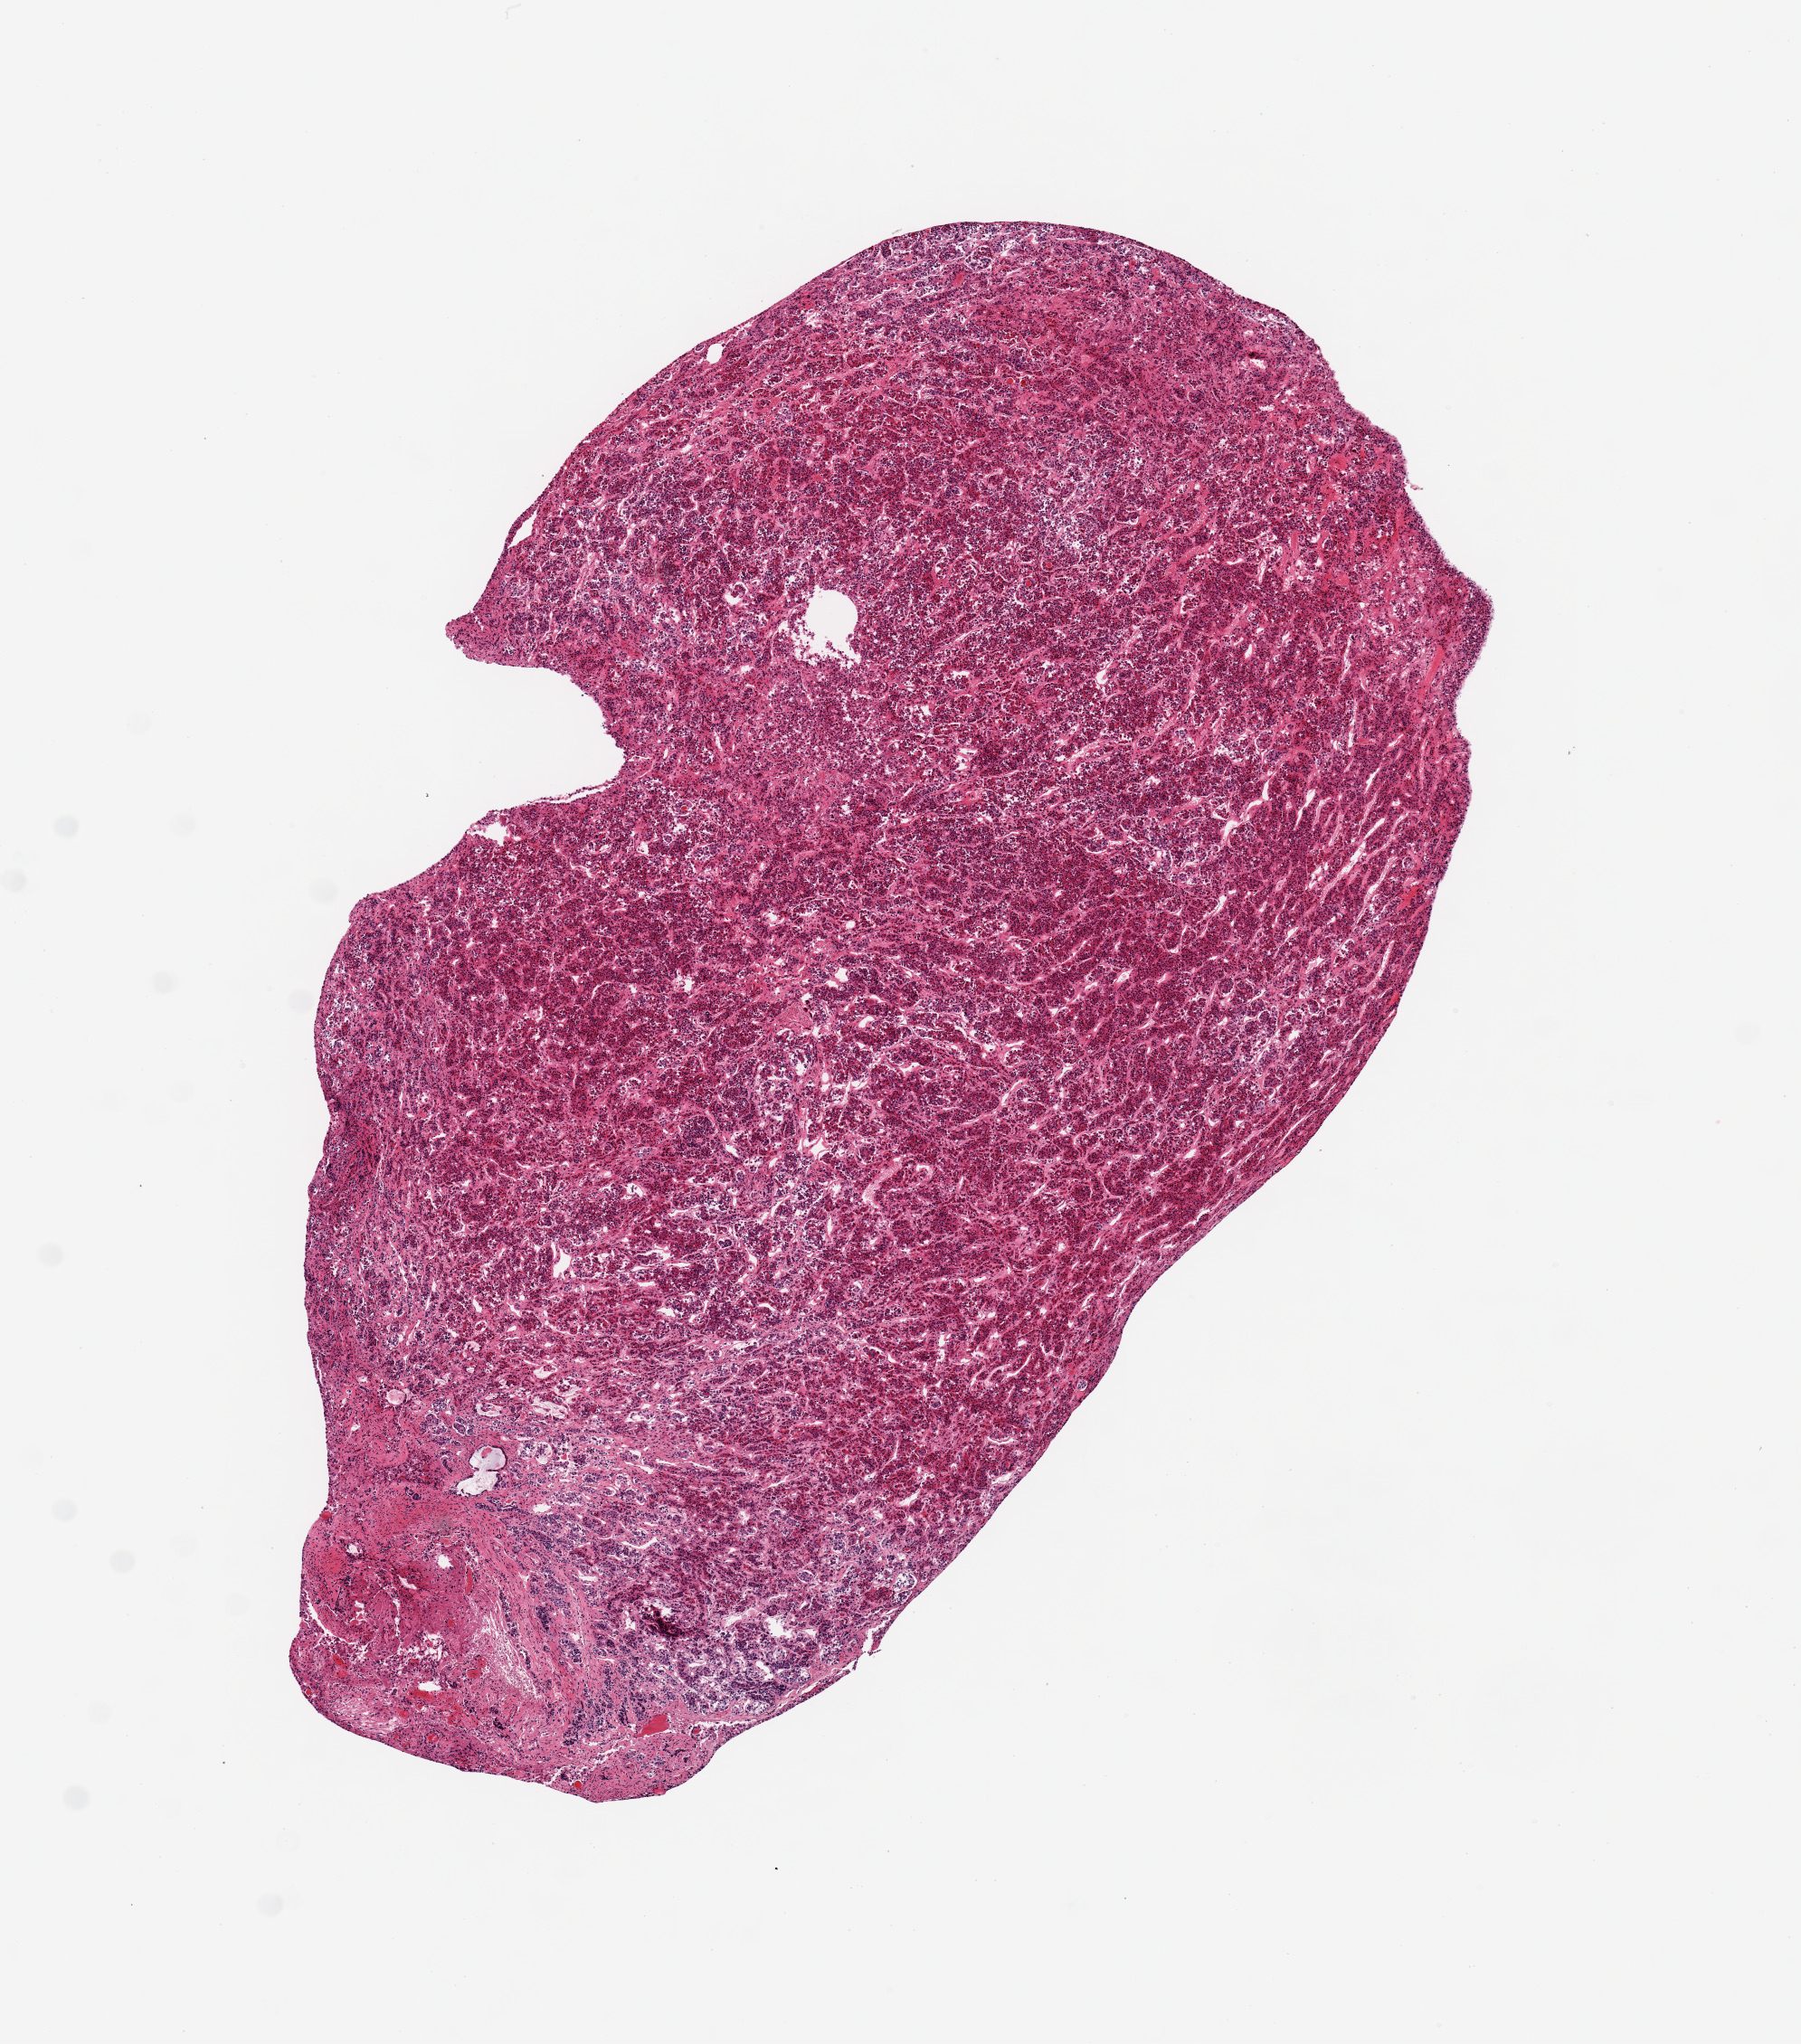
Whole-slide image, haematoxylin and eosin stain, low-resolution overview of the scanned area, about 7.9 x 8.9 mm, PAXgene-fixed, paraffin-embedded tissue, target tissue: pituitary, donor tissue sample.
Review note (as recorded): 1 piece ~7x4mm. Adenohypophysis only.